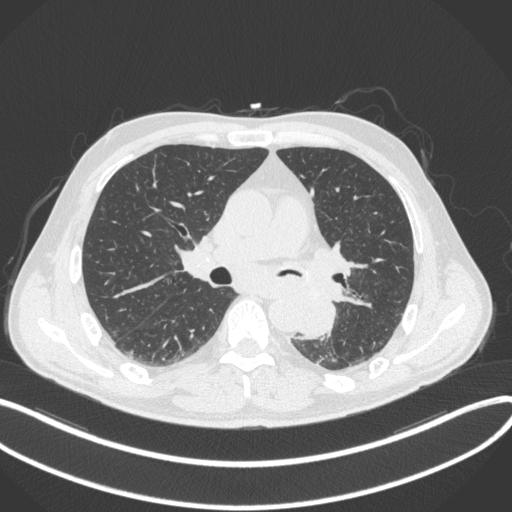
Chest CT, one axial slice; reconstruction kernel B31f; 120 kVp; lung window (W 1500 / L -600 HU); 1 mm slice thickness; 512 × 512 image matrix. Patient: male, 59 years. Case-level facts recorded for this patient, not image findings: clinical TNM (as recorded): T2a N2 M0.
Annotated regions visible in this slice (rectangle marked by the reading radiologist):
- lung tumour (recorded histology: squamous cell carcinoma): bounding box [x1, y1, x2, y2] px = [299, 289, 340, 340]